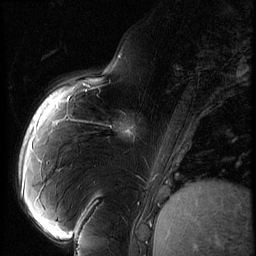
Breast MRI (dynamic contrast-enhanced), one sagittal slice. Position 19 of 60 along the scan axis. 3 images stored at this slice position (order not interpretable as contrast timing). 1.5 T. TE 4.2 ms, TR 9 ms. 2.5 mm slice thickness. 256 × 256 image matrix, field of view 180 × 180 mm. Female patient, age 57 years. Case-level facts recorded for this patient, not image findings: setting: breast cancer imaged before/during neoadjuvant chemotherapy; receptor status: triple-negative.
Annotated regions visible in this slice (semi-automatically segmented with operator editing):
- analysis volume of interest (the breast-tissue region the enhancement analysis was run in; not a lesion): bounding box [x1, y1, x2, y2] px = [106, 101, 157, 152]
- tumour enhancement mask (voxels above the 140 % enhancement threshold inside the analysis volume of interest): [112, 127, 135, 132]